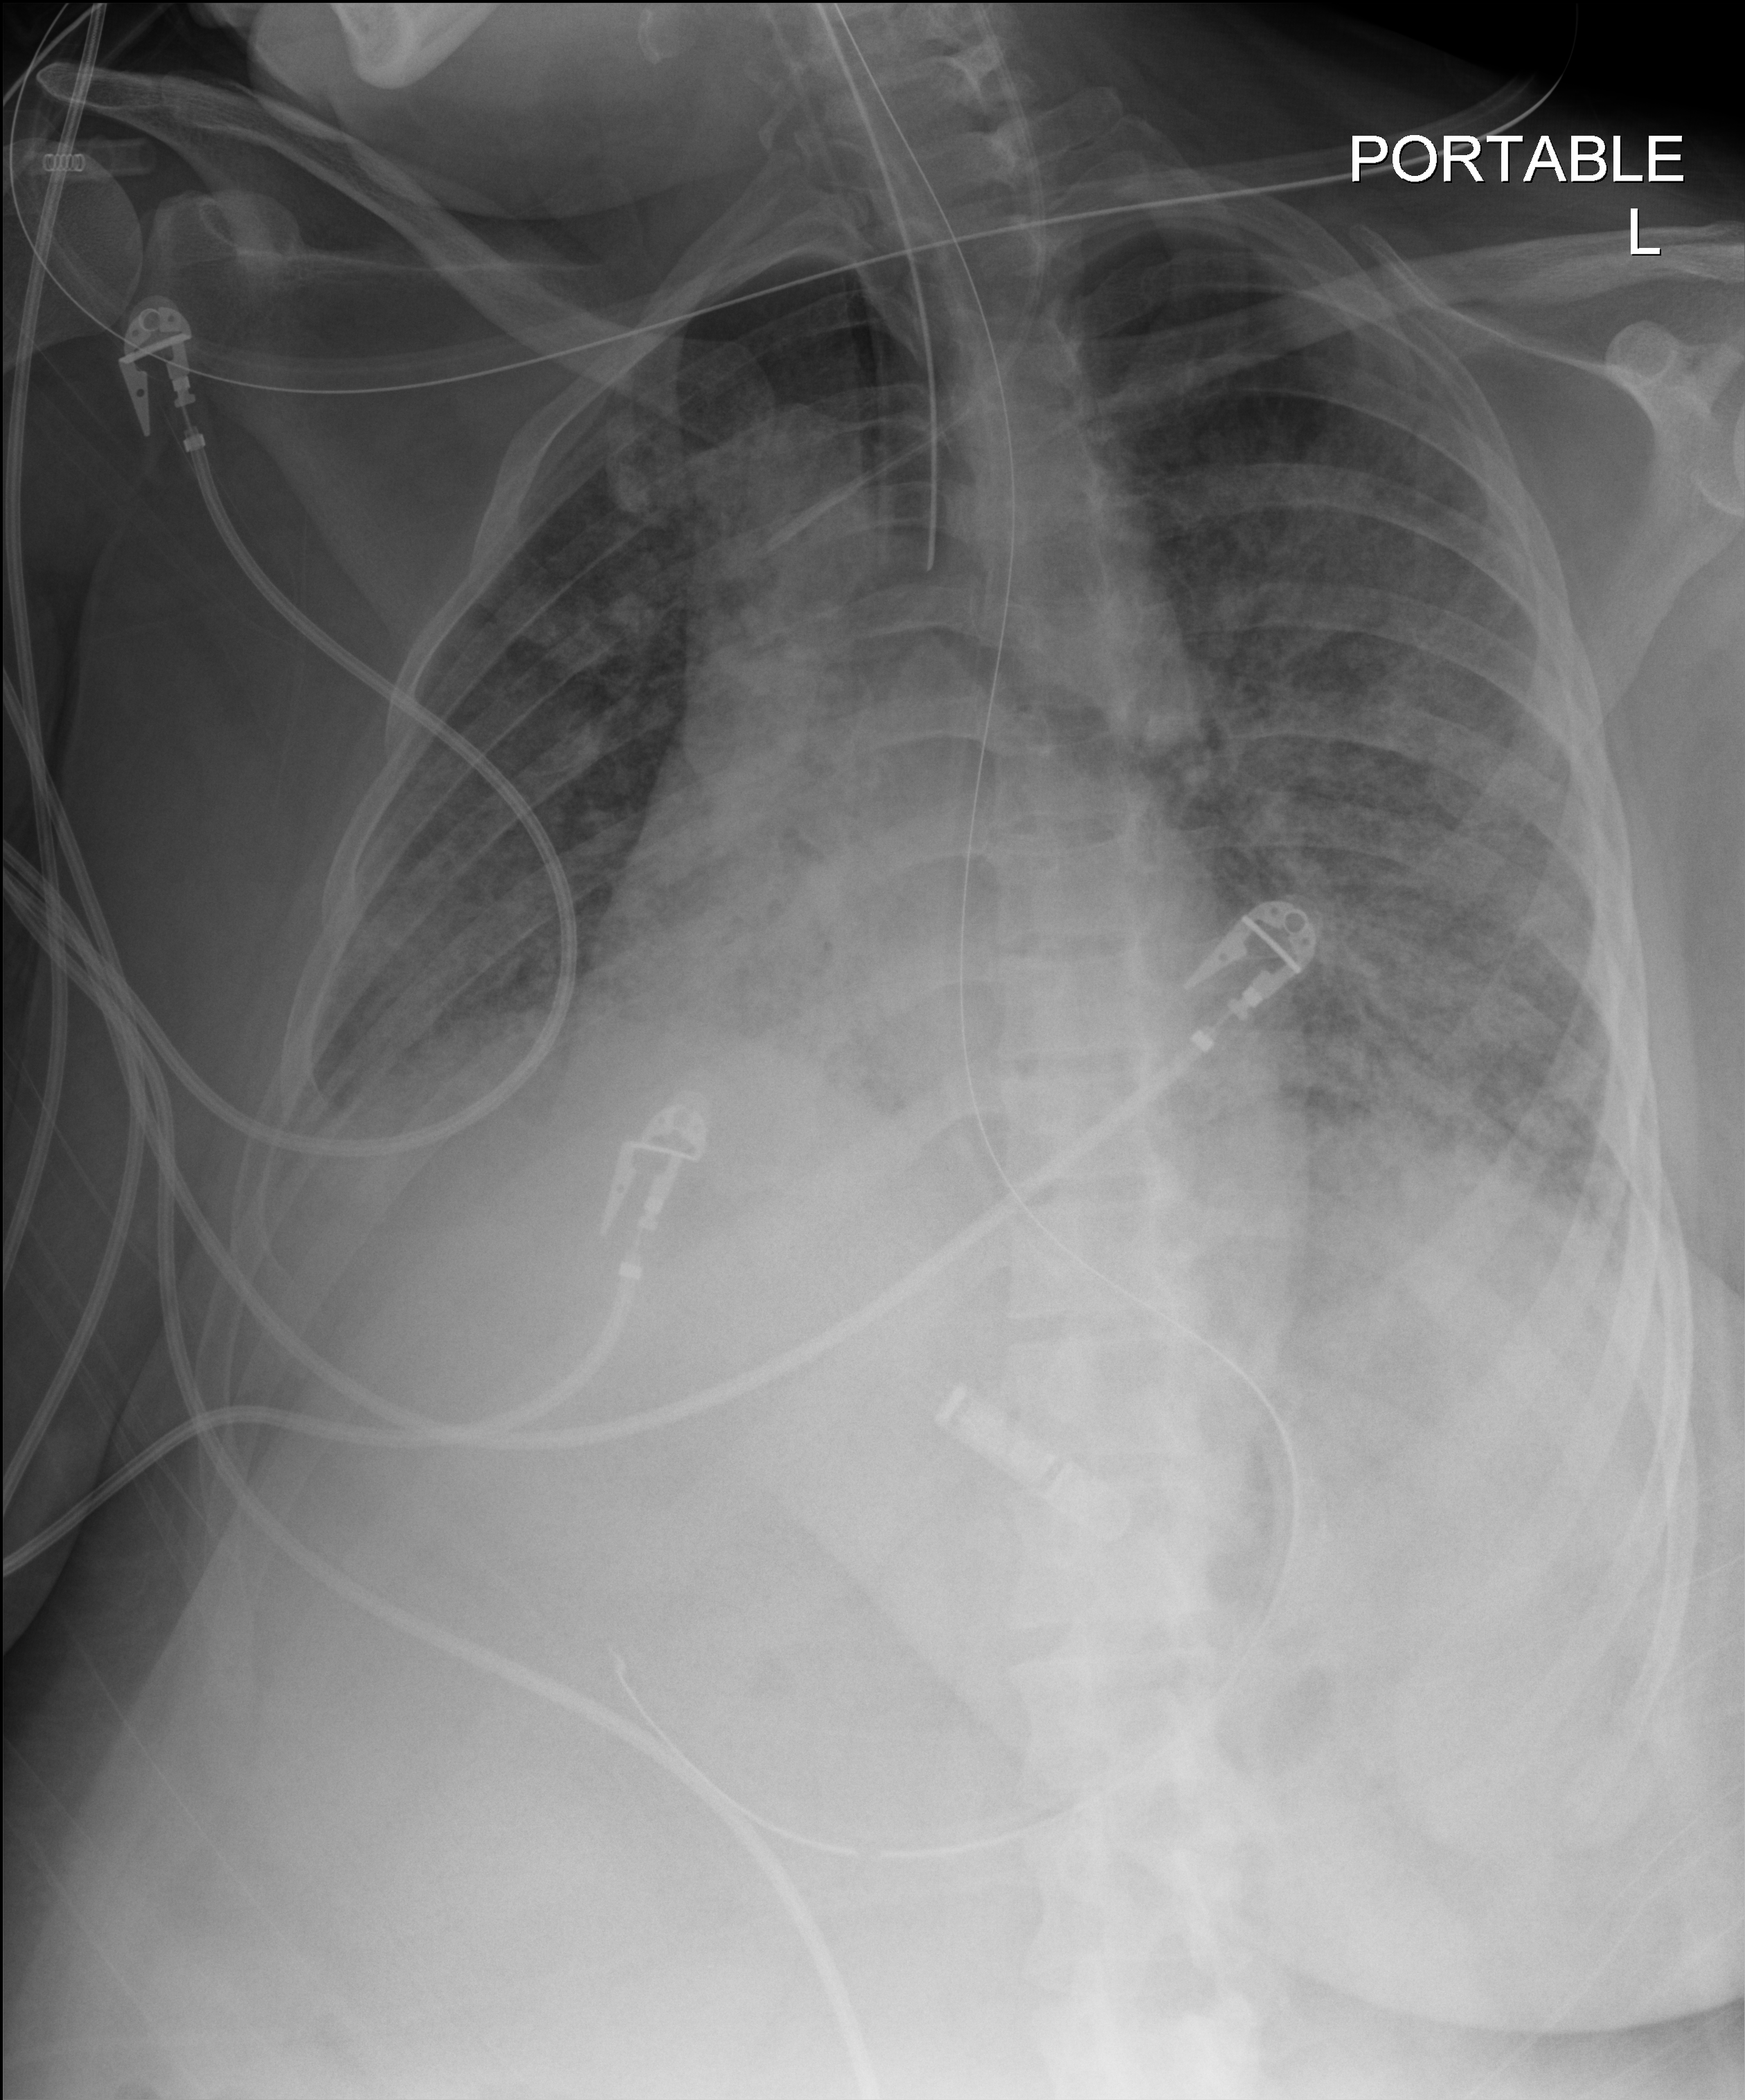
Chest X-ray; anteroposterior (AP) projection. Female patient hospitalised with COVID-19, age 18–59 years.
Hospital-stay facts (about this admission, not read from this image; timing relative to this image not recorded):
- admitted to intensive care during this hospital stay: no
- mechanically ventilated during this hospital stay: yes